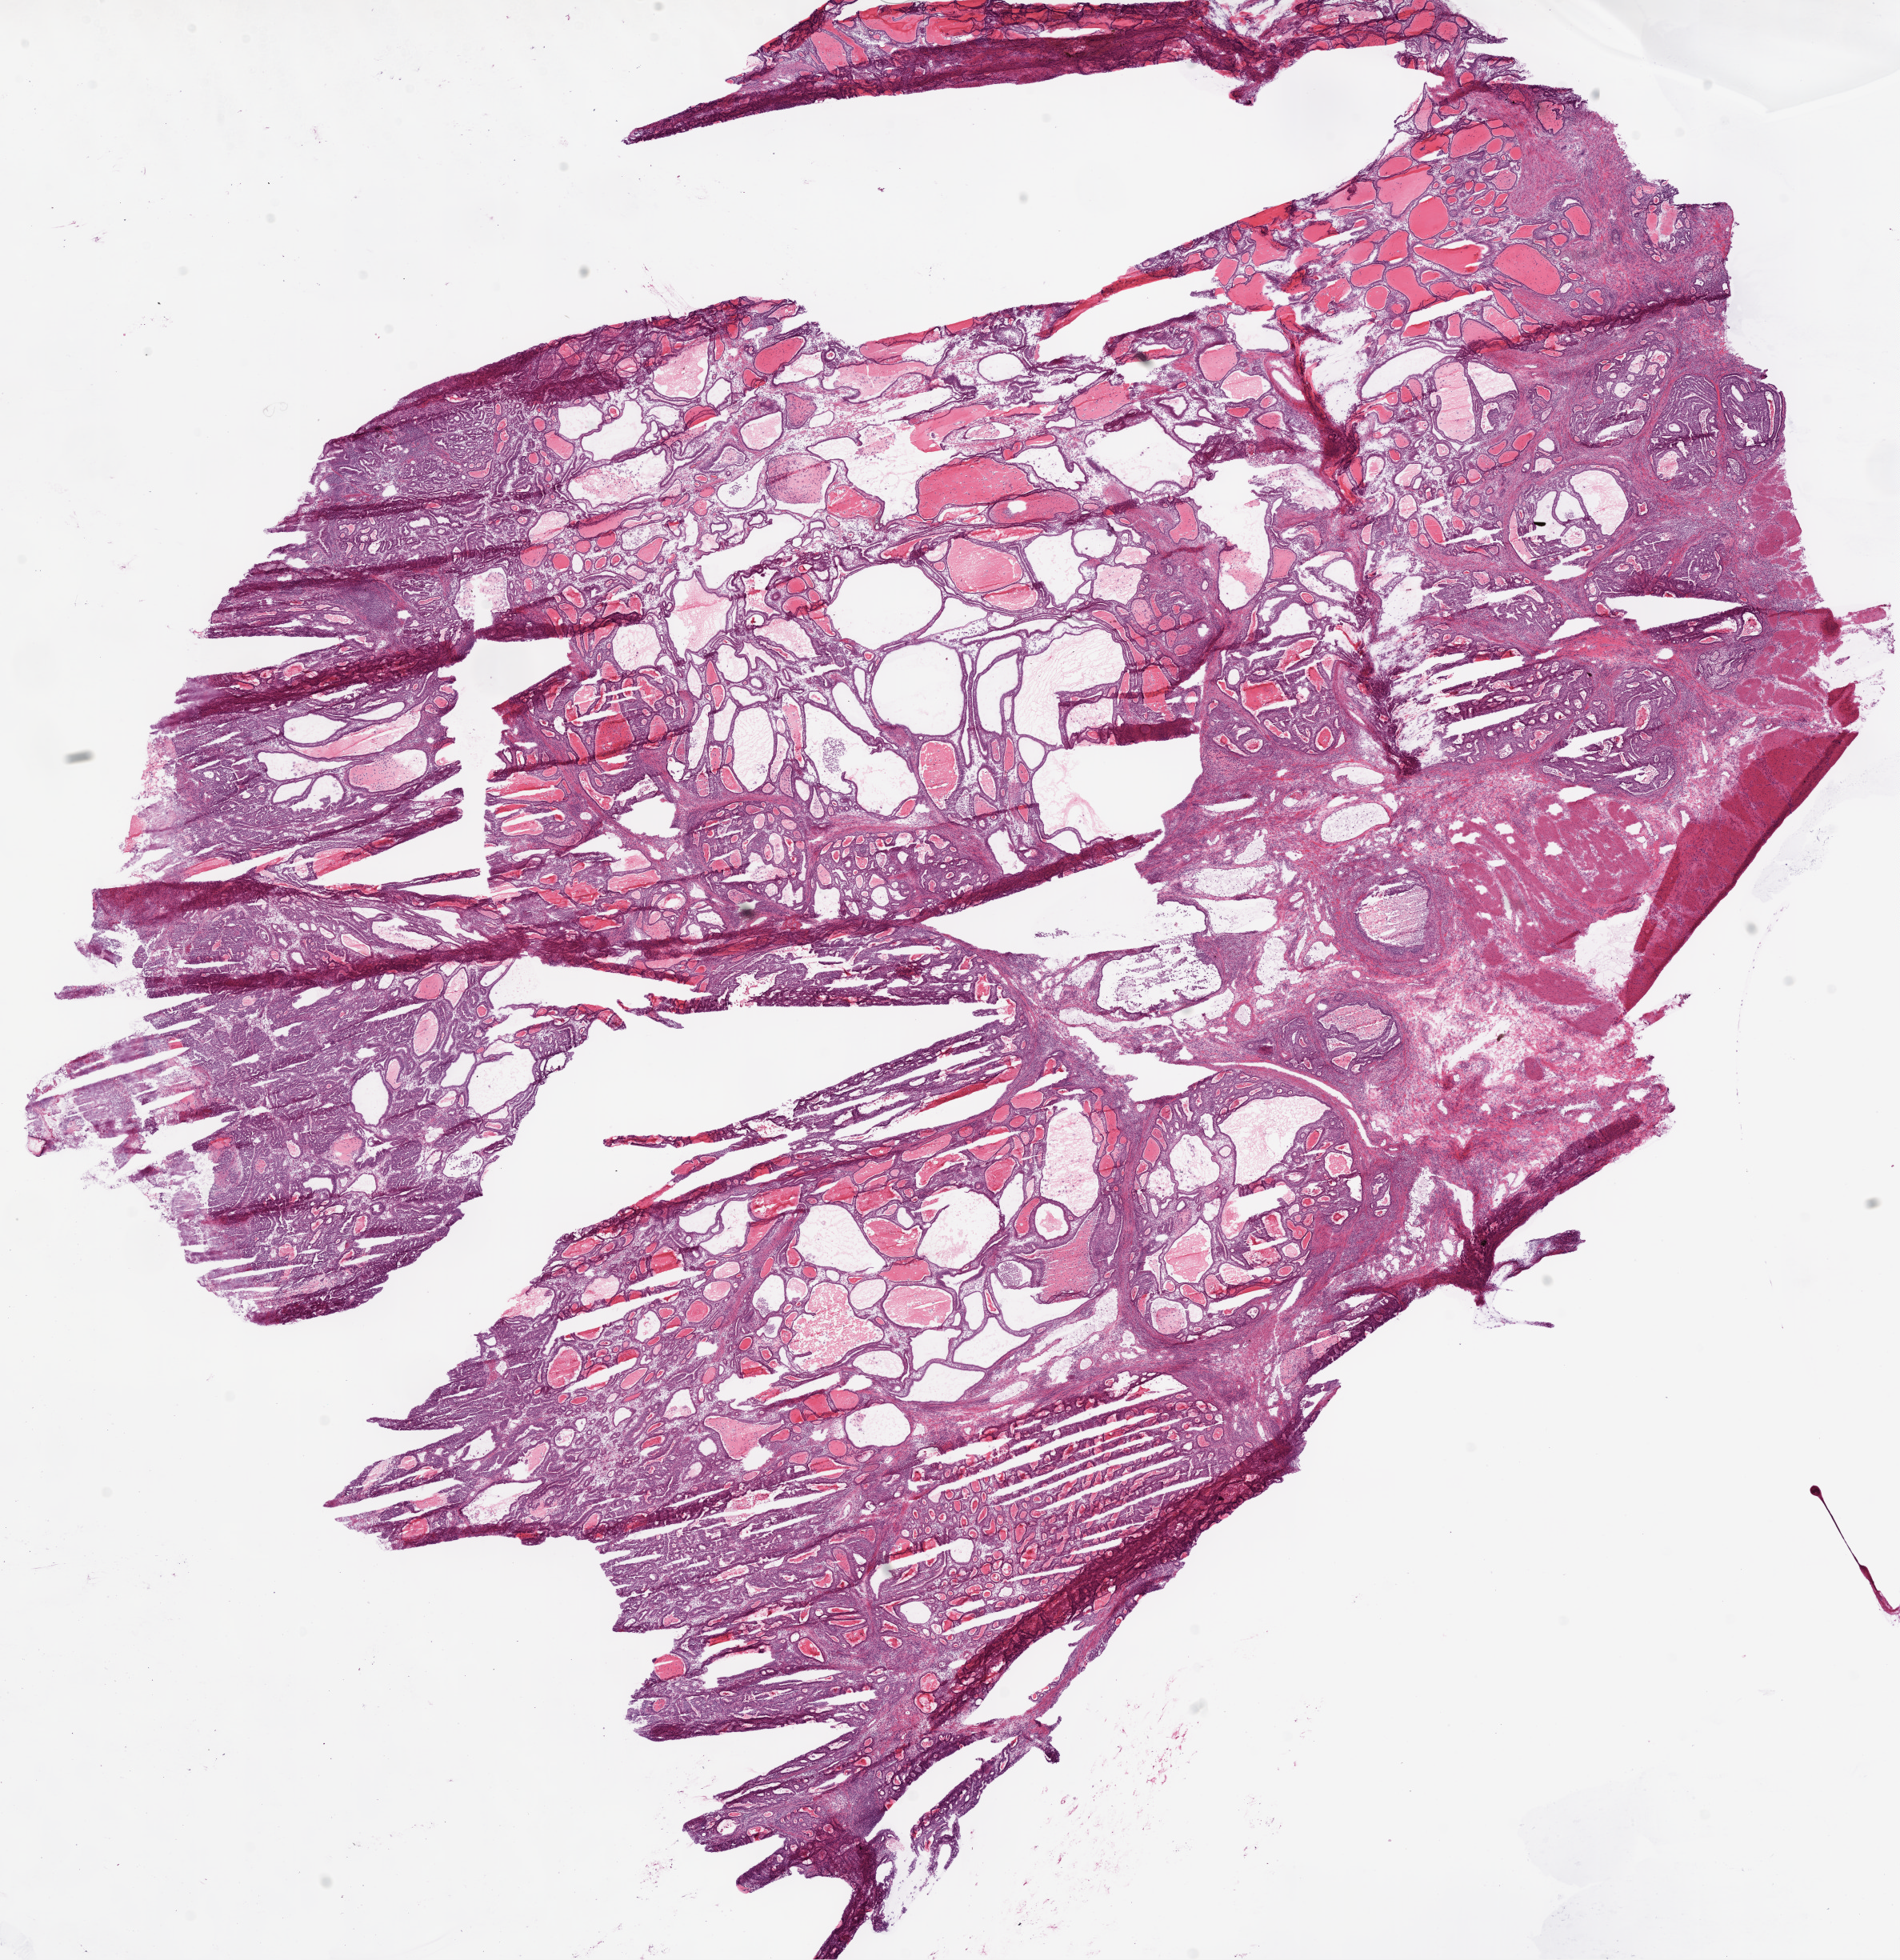
Whole-slide histology image, H&E-stained, shown as a low-resolution overview of the whole scanned area (about 19.1 x 19.7 mm, from a 20x scan), frozen section from the bottom of the tissue portion, stomach, primary tumour sample. Patient: male, age at initial diagnosis 72 years. Histologic grade: G2 (moderately differentiated). Pathologist review of this section (percent, as recorded): tumour cells 88%, tumour nuclei 85%, normal cells 5%, stromal cells 5%, necrosis 2%.
* pathologic diagnosis: Adenocarcinoma, NOS
* lymph nodes positive (case pathology): 3 of 8 examined